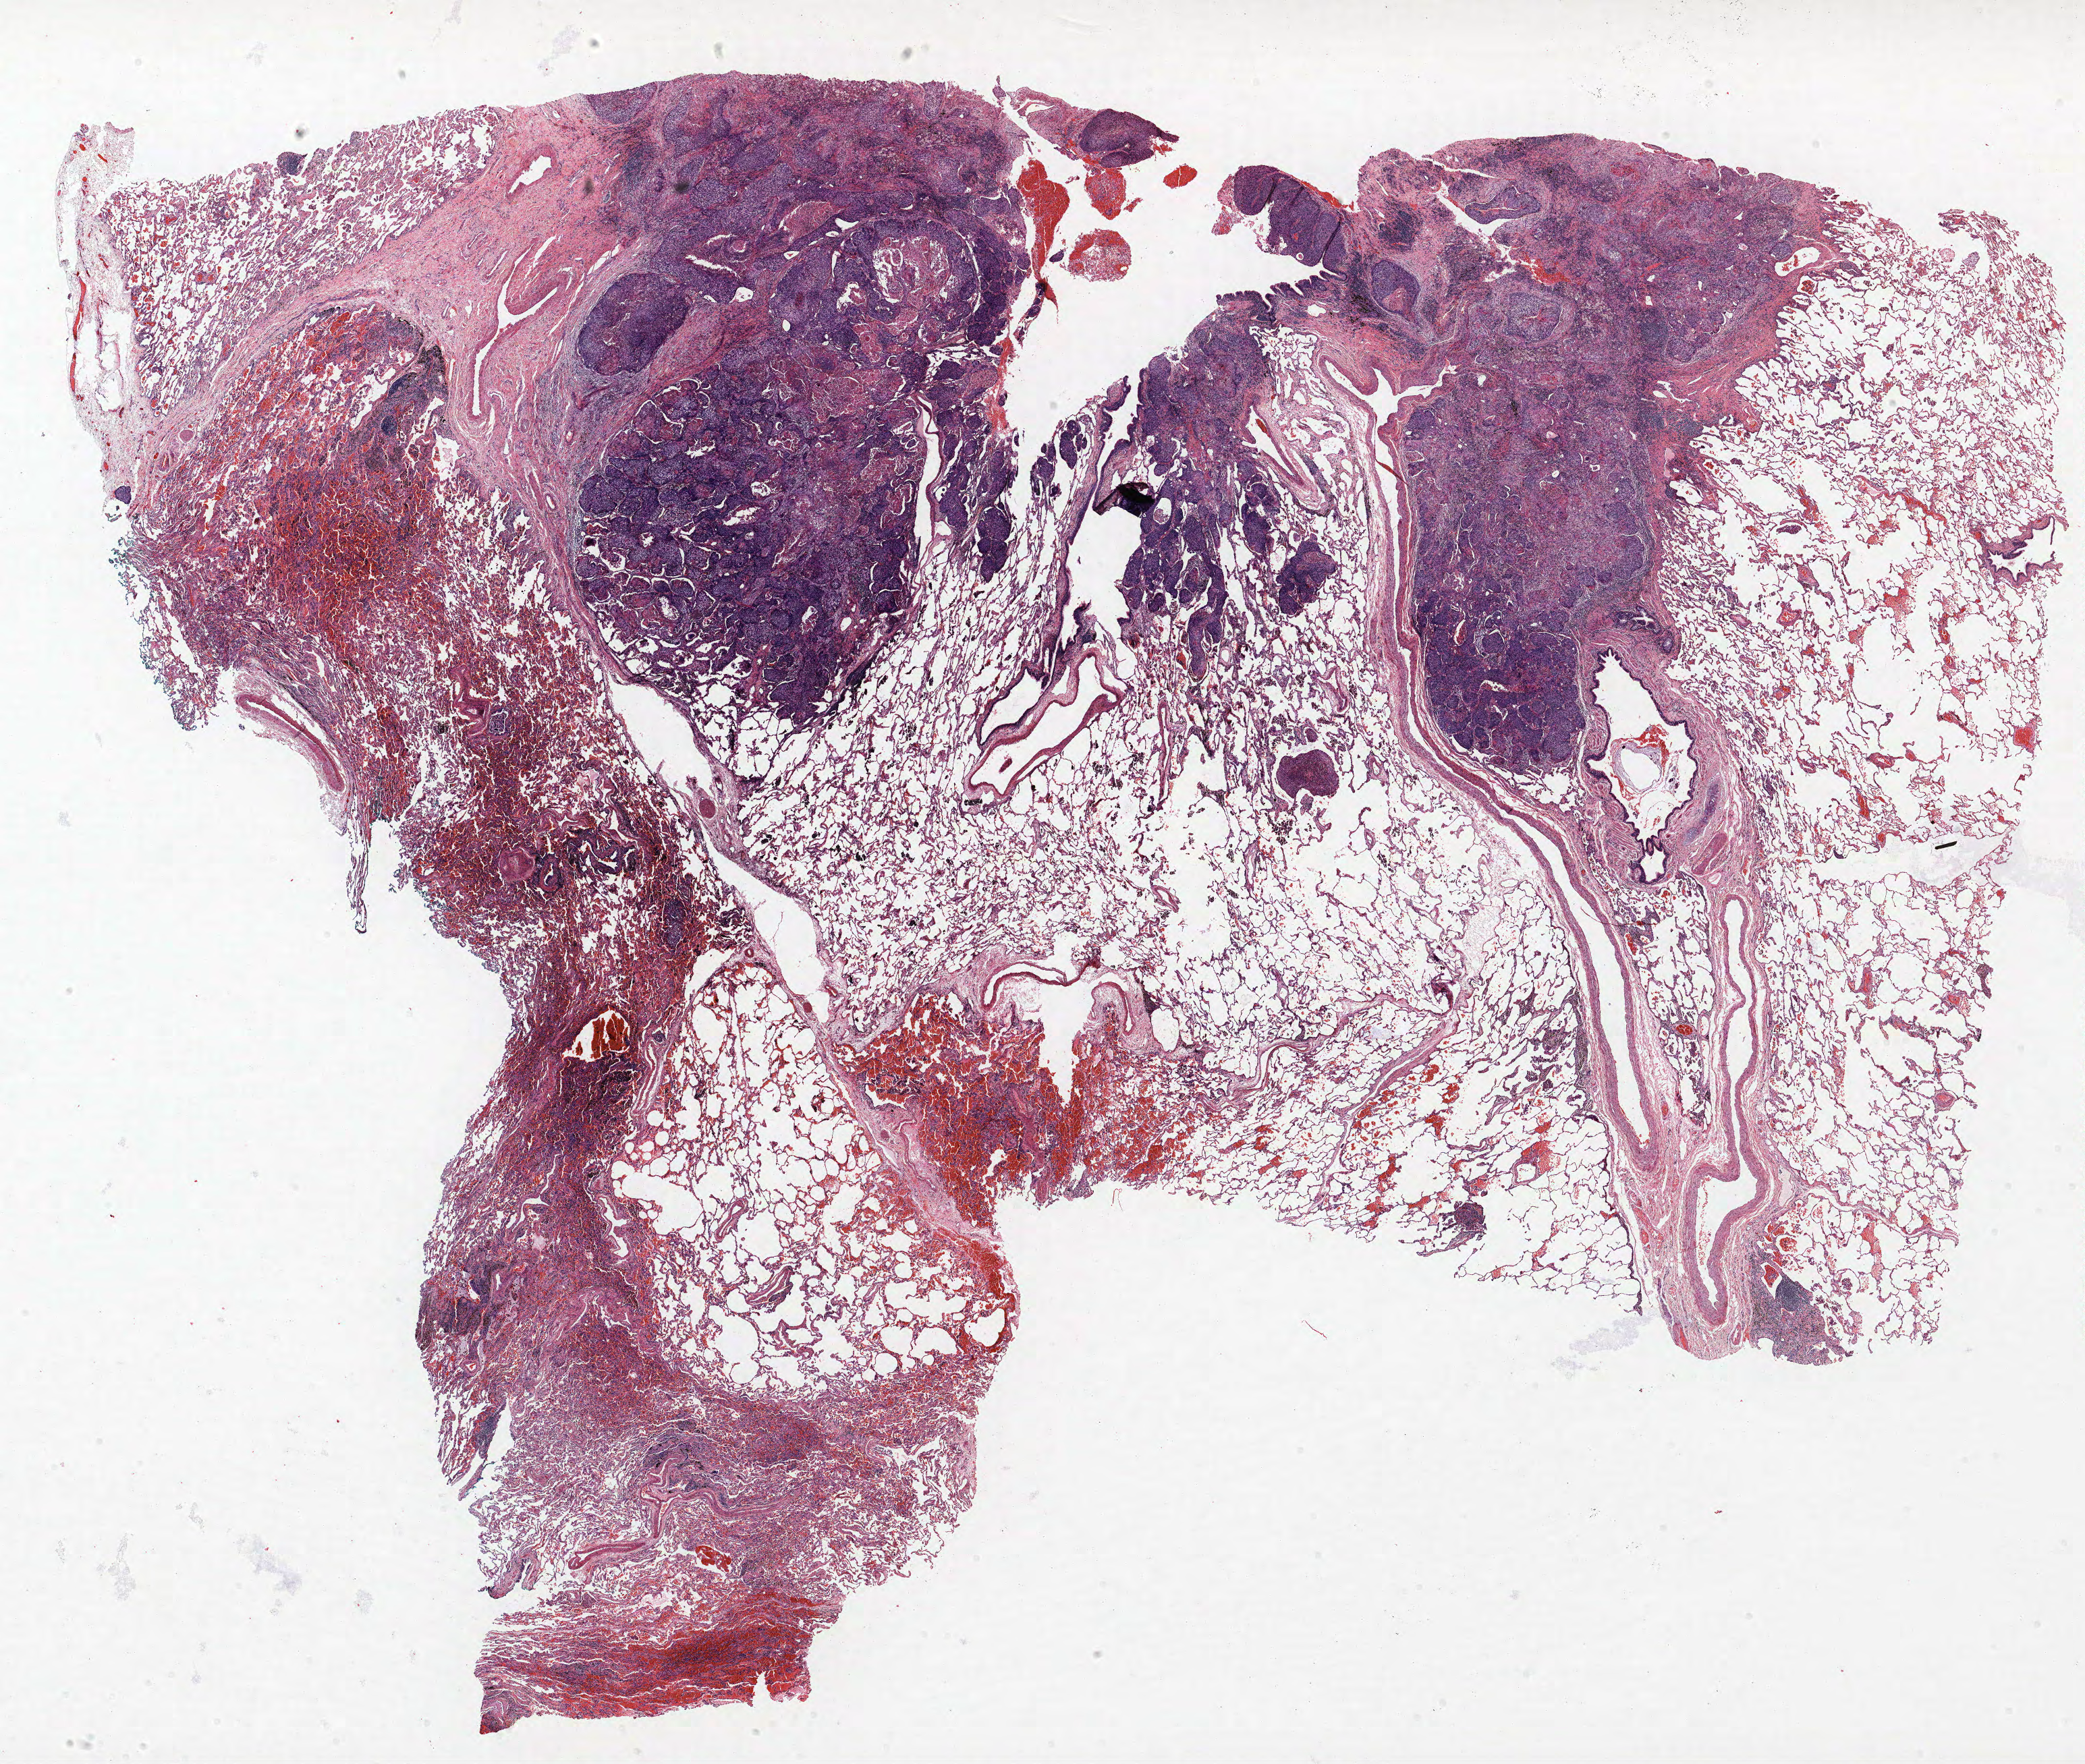
H&E whole-slide image, whole scanned area (about 24.7 x 20.9 mm, slide scanned at 40x) shown as a low-resolution overview, formalin-fixed paraffin-embedded (FFPE) section, lung. Male, age 57 at enrolment. Current smoker at enrolment. Grade: moderately differentiated (G2).
• stage (AJCC 6th edition): IB
• participant's lung-cancer diagnosis: Squamous cell carcinoma, NOS
• tumour size (pathology): 18 mm
• primary tumour location (clinical record): right middle lobe
• note: participant had 2 primary lung cancers recorded; fields above describe the first